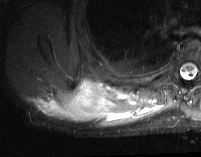
MRI of an extremity soft-tissue mass, one axial slice; position 20 of 74 along the scan axis; STIR; MR volume resampled by the dataset authors to the PET/CT grid (not the native acquisition matrix); 3.27 mm slice thickness; 201 × 157 image matrix, field of view 196 × 153 mm. Male patient. From the clinical record (not read from this slice): histological type: pleiomorphic spindle cell undifferentiated; grade: high; site of the primary tumour: right parascapusular.
Outlined on this slice (expert contour drawn on MRI and transferred to this co-registered scan by the dataset authors):
- gross tumour volume including surrounding oedema: bounding box (x1, y1, x2, y2) in pixels: (35, 78, 162, 129)
- gross tumour volume (mass): (60, 82, 111, 120)